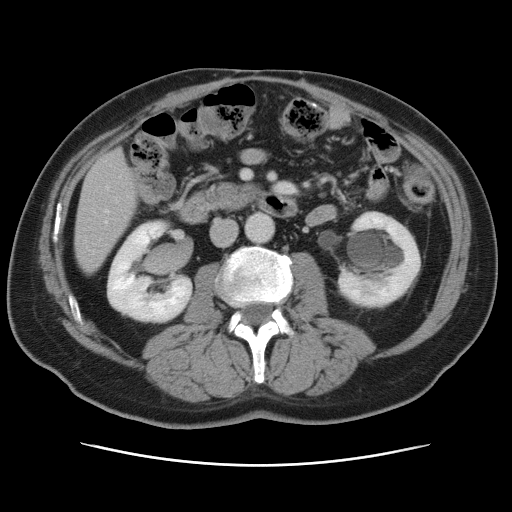
Contrast-enhanced abdominal CT, one axial slice; position 22 of 80 along the scan axis; intravenous contrast given; soft-tissue window (W 400 / L 40 HU); 512 × 512 image matrix. Male patient, age 69 years. From the clinical record (not read from this slice): diagnosis: colorectal cancer liver metastases, imaged before liver resection; multiple liver metastases: no; largest metastasis: 5 cm; disease in both lobes: yes.
Structures marked on this image (expert manual segmentation):
- hepatic veins: bounding box [x1, y1, x2, y2] px = [106, 187, 108, 212]
- liver: [75, 151, 137, 271]
- planned liver remnant (the part of the liver to remain after resection): [75, 223, 122, 272]